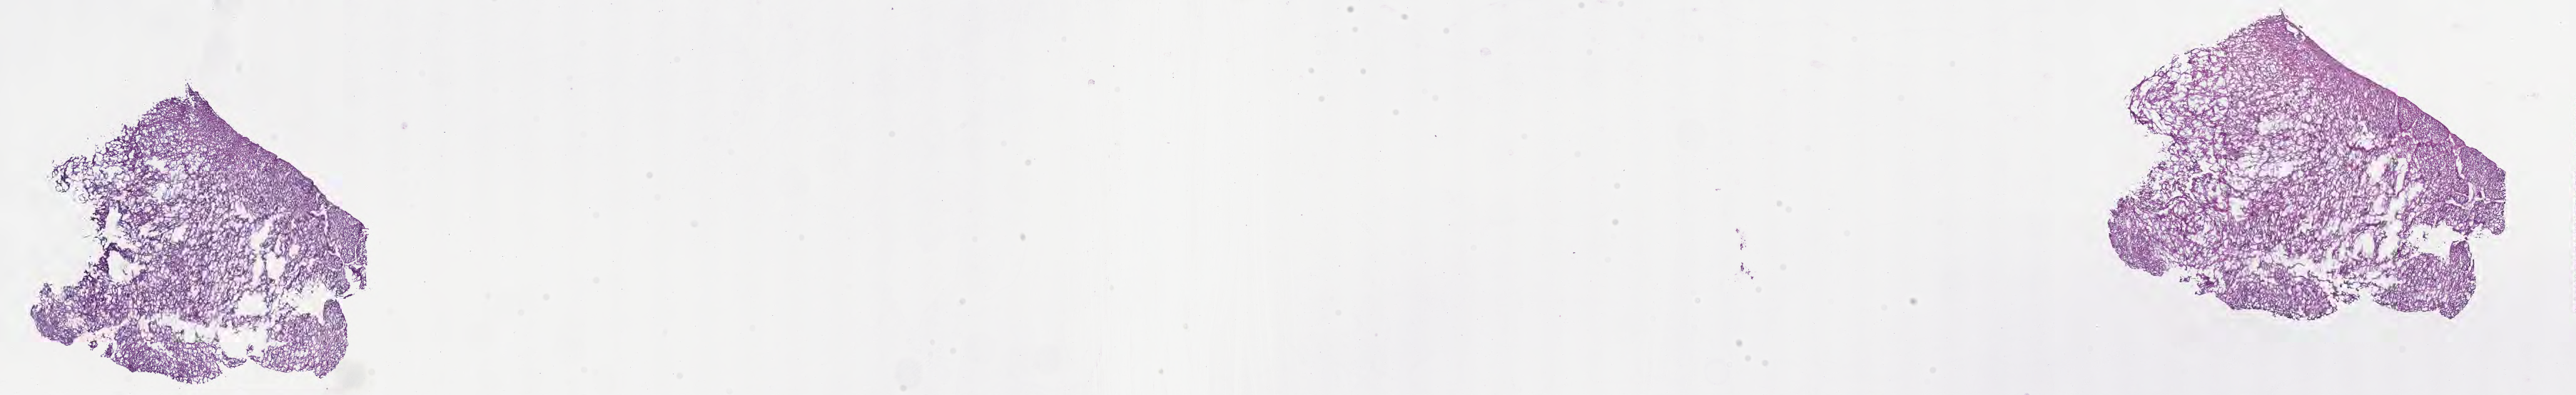
Hematoxylin and eosin (H&E) whole-slide image of tumor tissue from the brain — low-resolution overview of the scanned area, about 29.2 x 4.5 mm; frozen section (OCT-embedded). Patient: female, age 649 days (about 1.8 years).
• diagnosis: Ependymoma, NOS